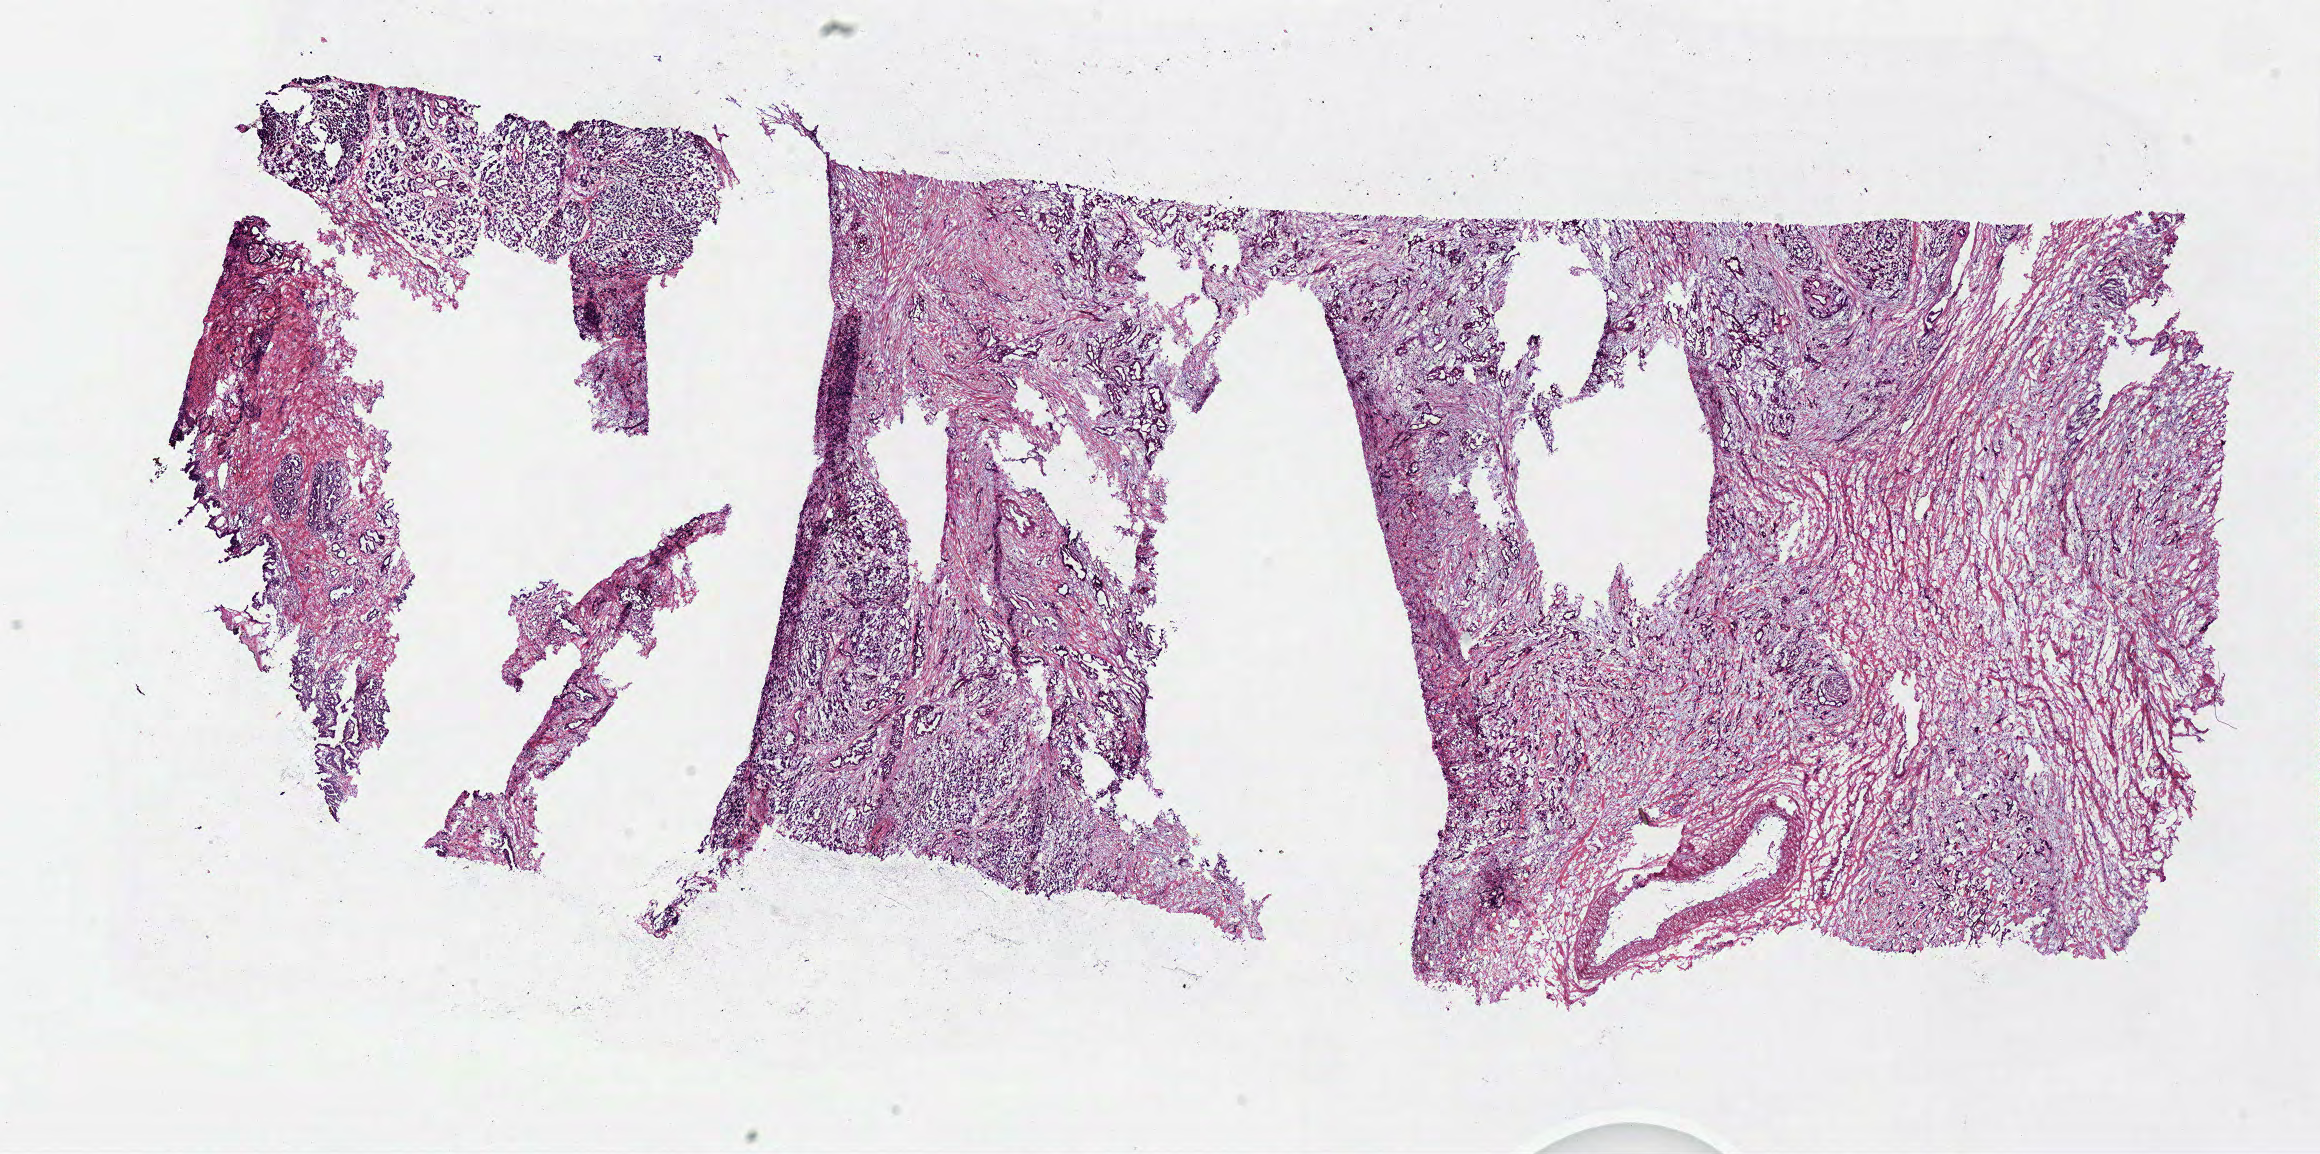
Whole-slide histology image, H&E-stained, low-resolution overview of the scanned area, about 18.3 x 9.1 mm (from a 40x scan). Frozen section from the top of the tissue portion. Sample: primary tumour, pancreas. Patient: male, age at initial diagnosis 52 years. Histologic grade: G3 (poorly differentiated). Pathologist review of this section (percent, as recorded): tumour cells 65%, tumour nuclei 70%, normal cells 5%, stromal cells 30%, necrosis 0%.
Histologic diagnosis: Infiltrating duct carcinoma, NOS (head of pancreas). AJCC pathologic stage: IIB. TNM: T3 N1 M0. Lymph nodes positive (case pathology): 3 of 9 examined.